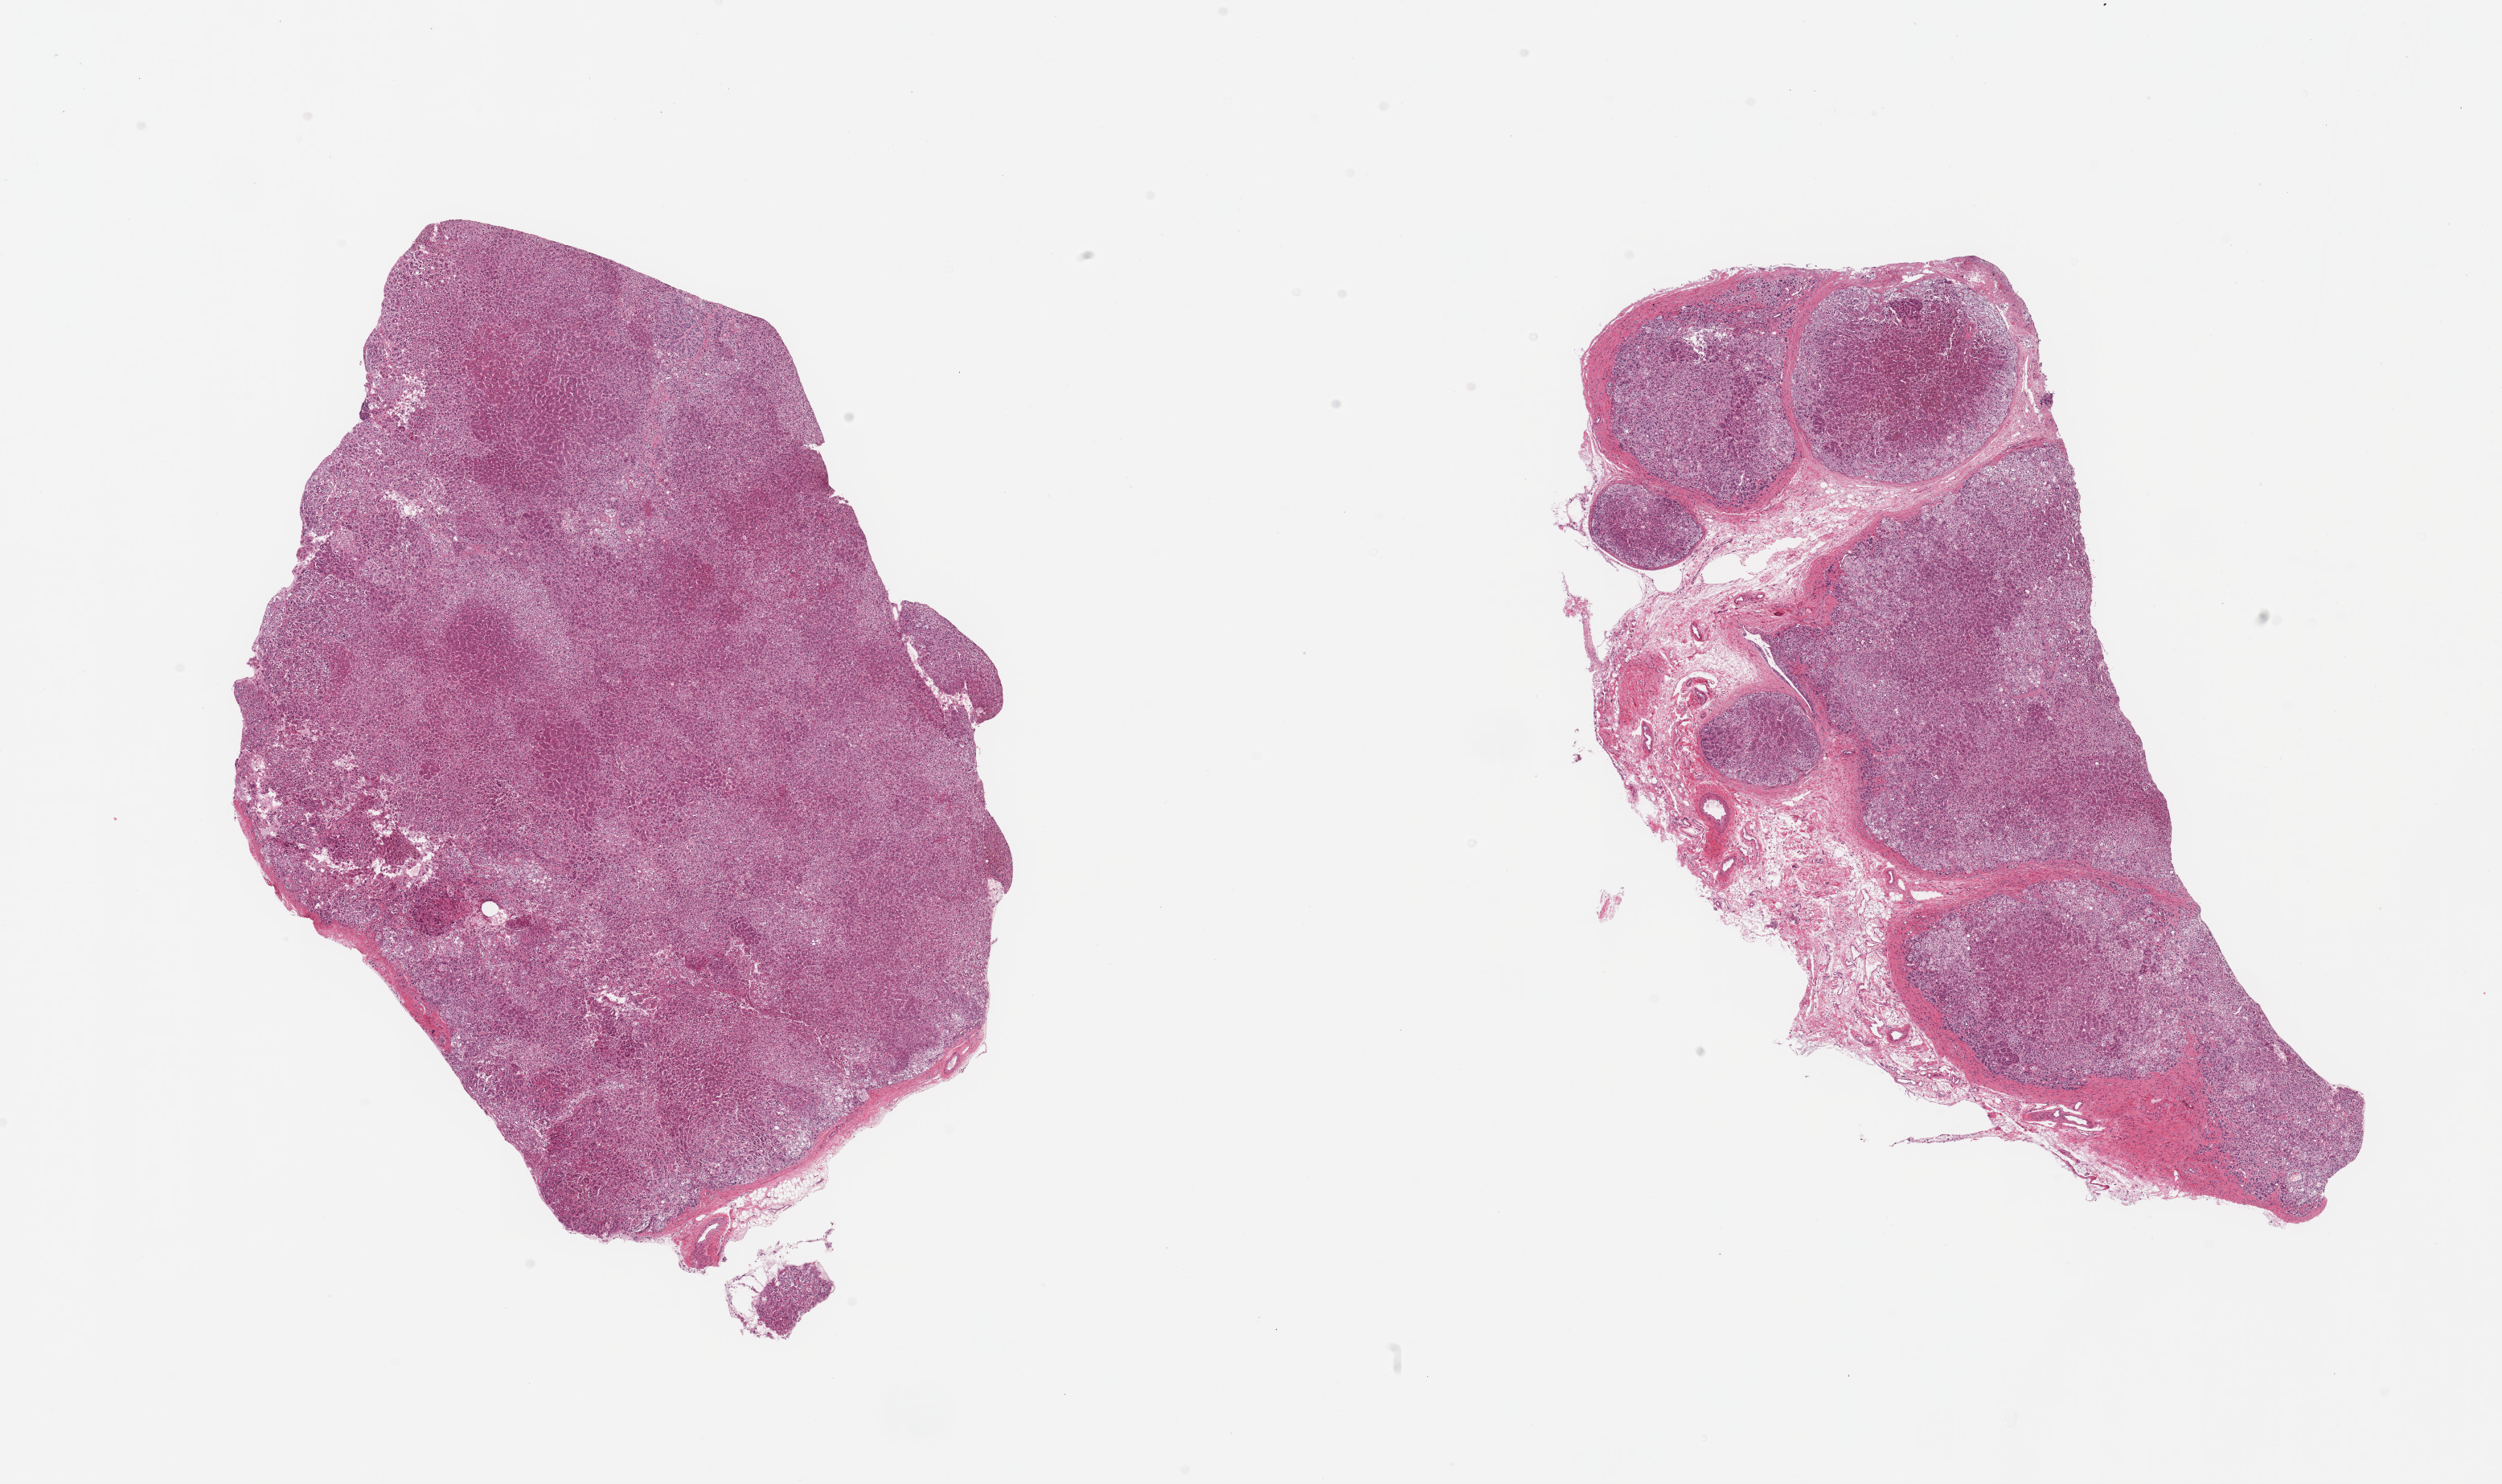
Haematoxylin and eosin whole-slide image — low-resolution overview of the scanned area, about 24.6 x 14.6 mm, PAXgene-fixed, paraffin-embedded tissue, sampled site (target tissue): adrenal gland, tissue donor sample. Donor: male.
Review note (as recorded): 2 pieces, cortex, ~10% adherent fat/vascular elements.